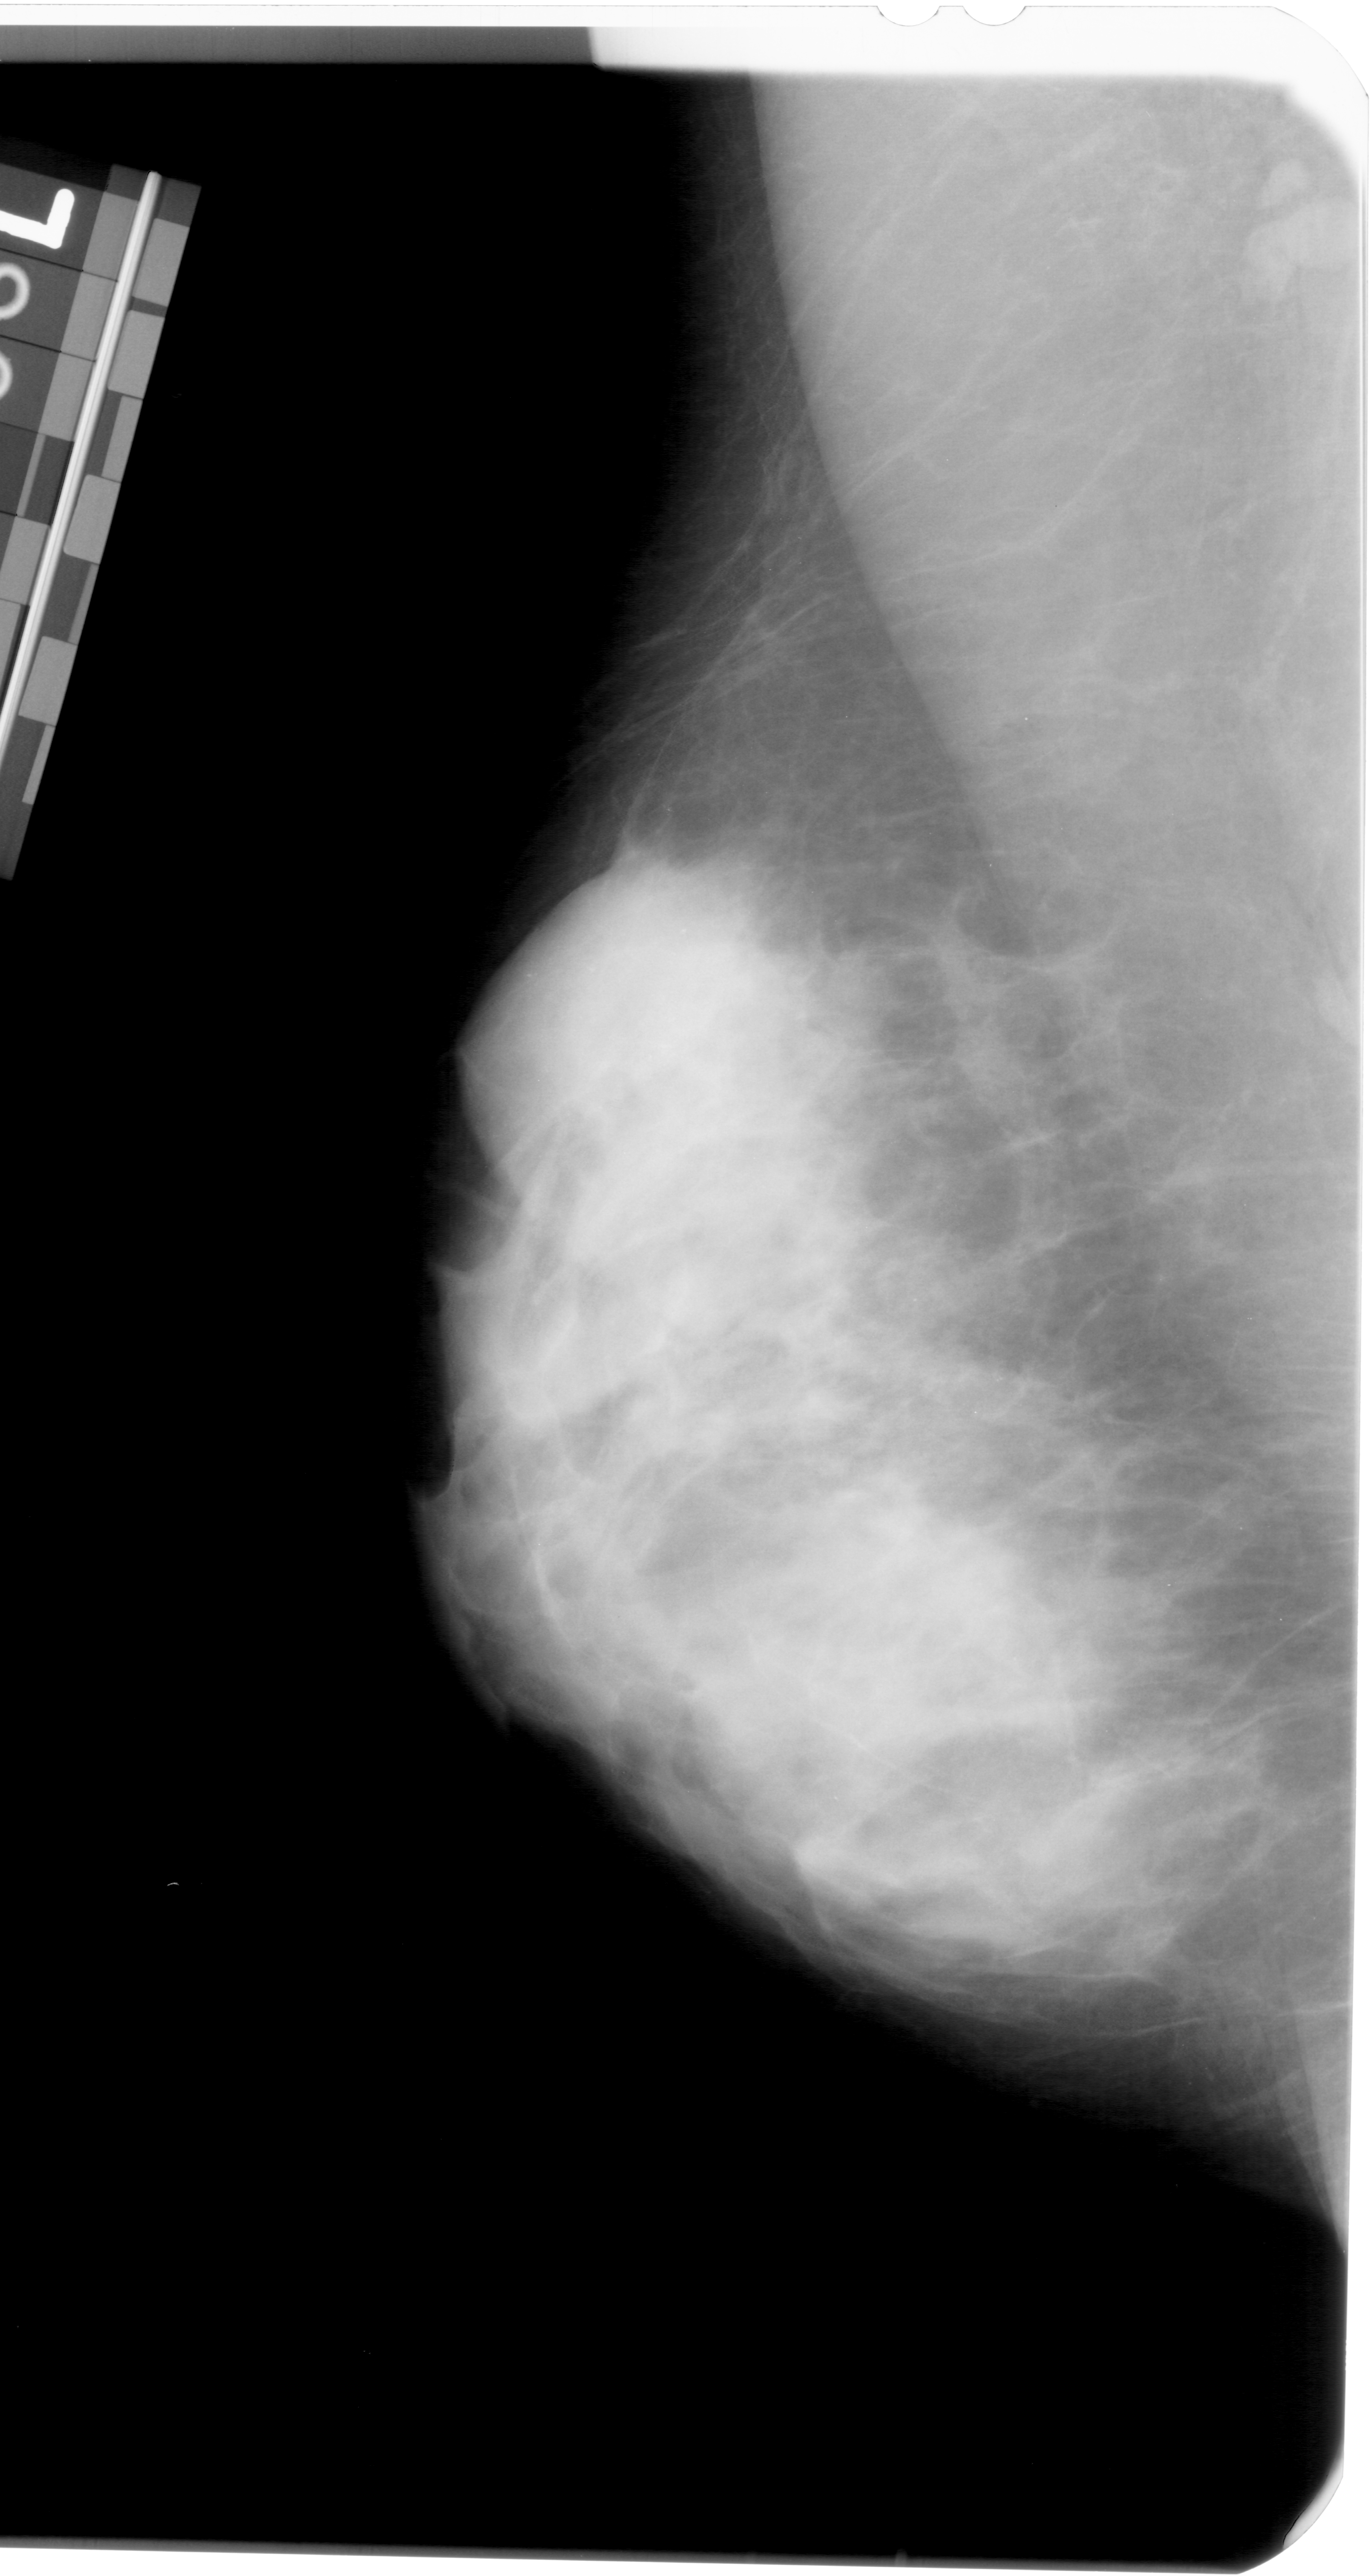
Mammogram (digitized film), left breast, mediolateral oblique (MLO) view, BI-RADS breast density category 4 (scale 1–4).
Marked findings (only marked abnormalities are described; nothing is implied about the rest of the image): calcifications, morphology pleomorphic, distribution segmental; BI-RADS assessment category 4; pathology (as recorded): benign.